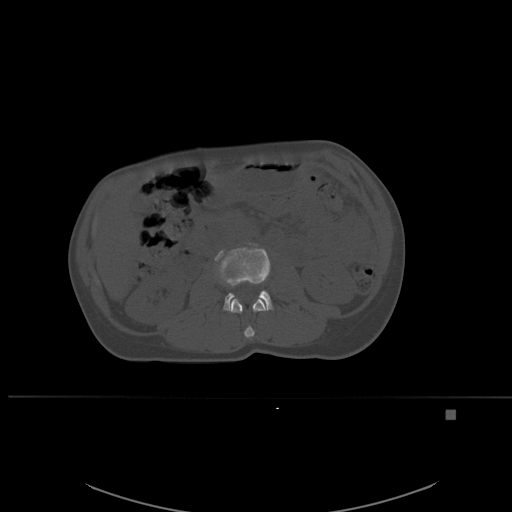
CT including the spine, one axial slice. Position 224 of 537 along the scan axis. Bone window (W 1800 / L 400 HU). 512 × 512 image matrix. Patient: female, 45 years. Case-level facts recorded for this patient, not image findings: primary cancer: lung.
Structures marked on this image (semi-automatic segmentation, software-assisted and operator-edited):
- L2 vertebra: box from (x=231, y=298) to (x=267, y=340) px
- L3 vertebra: (x=214, y=243)–(x=273, y=312)